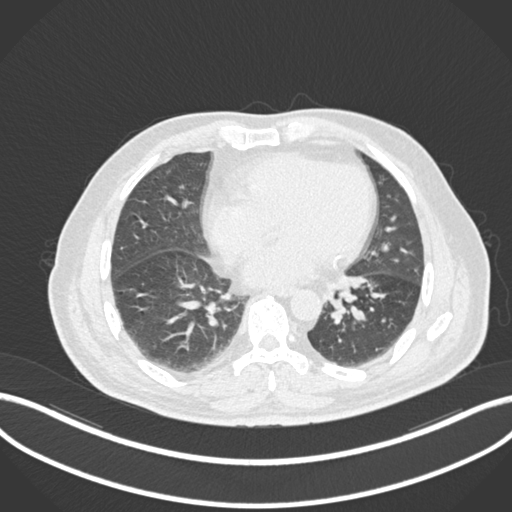
Chest CT, one axial slice. Slice 40 of 161 in the series (ordered by position). 120 kVp. Lung window (W 1500 / L -600 HU). 1 mm slice thickness. 512 × 512 image matrix, field of view 400 × 400 mm. Male patient, age 71 years. From the clinical record (not read from this slice): clinical TNM (as recorded): T1b N0 M0.
Annotated regions visible in this slice (bounding box drawn by a radiologist):
- lung tumour (recorded histology: squamous cell carcinoma): box from (x=326, y=287) to (x=351, y=325) px